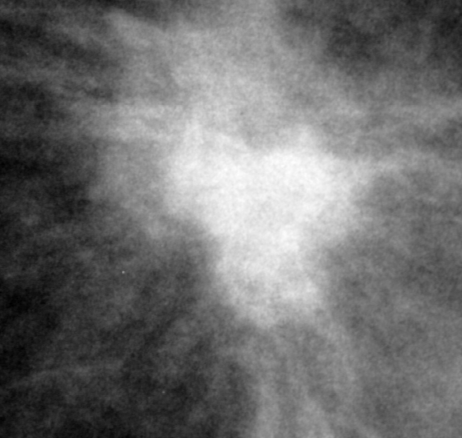
Crop from a digitized film mammogram around one marked abnormality, left breast, CC view.
Marked abnormality: mass, shape irregular, margins spiculated; BI-RADS assessment category 5; pathology (as recorded): malignant.